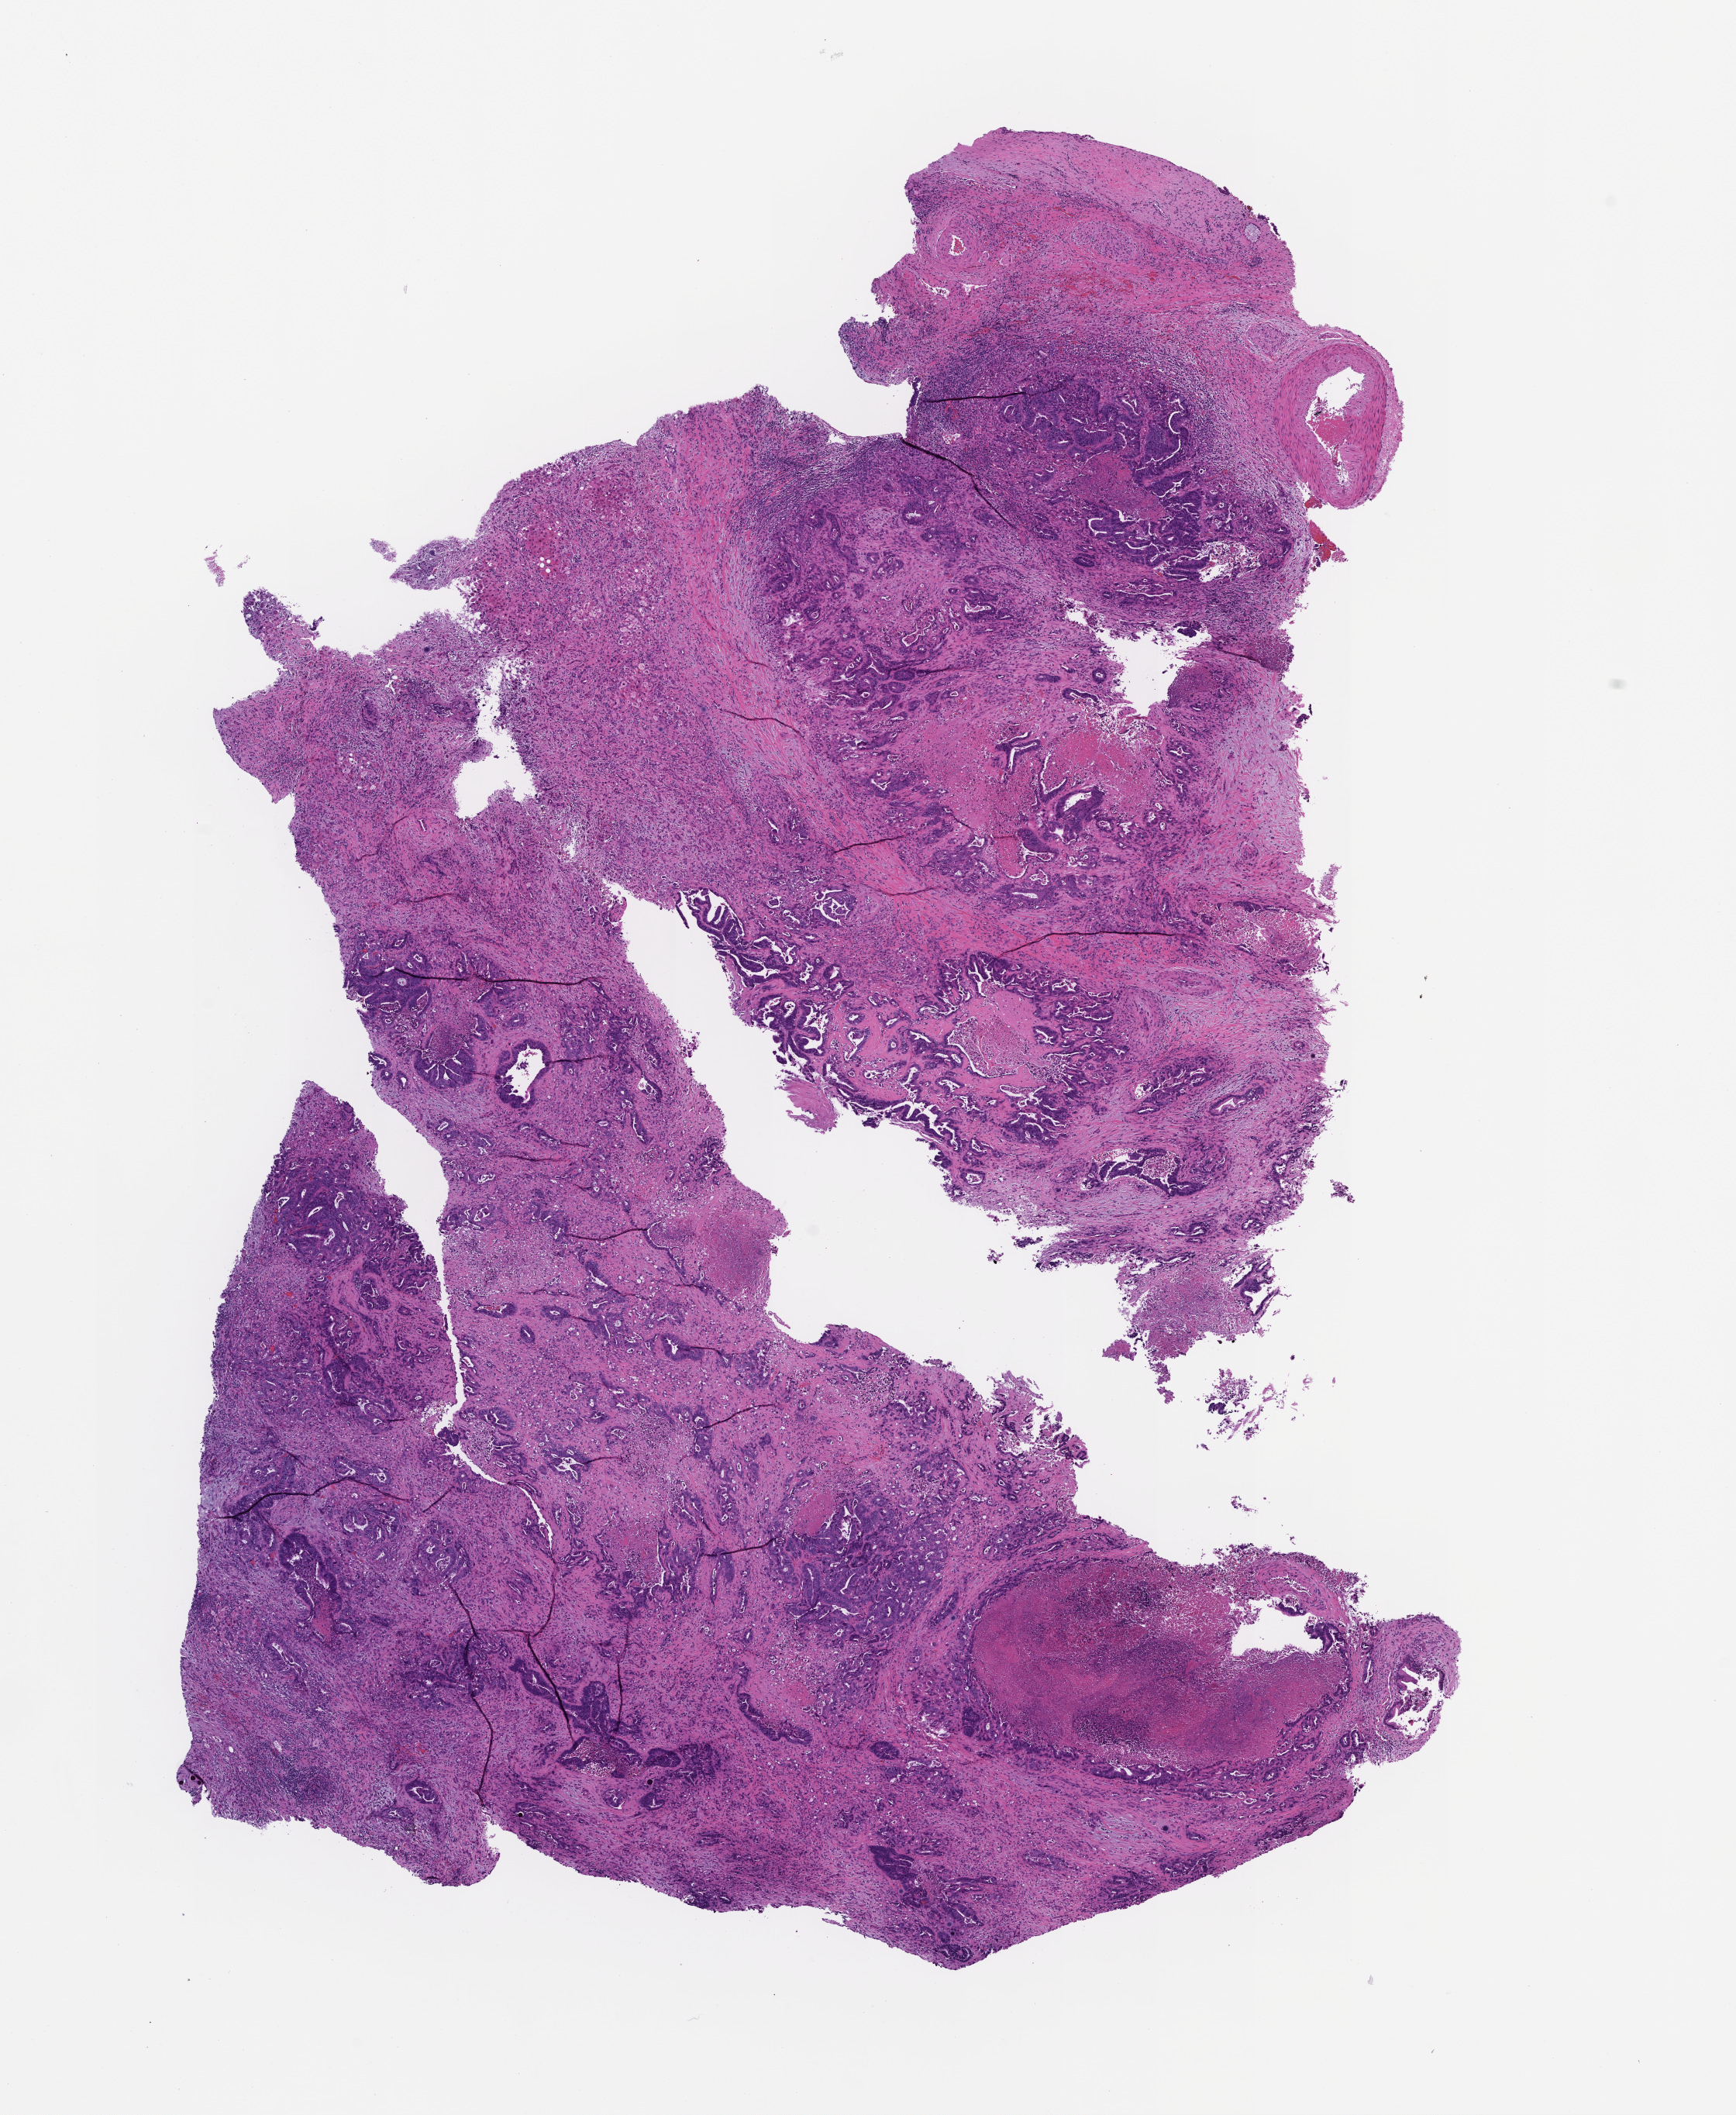
Haematoxylin and eosin whole-slide image, shown as a low-resolution overview of the whole scanned area (about 9.0 x 11.0 mm); formalin-fixed paraffin-embedded section; specimen time point: collected at baseline (before treatment). Patient sex: female.
- this section: metastasis (sampled organ not recorded)
- primary diagnosis of the patient: Colorectal Carcinoma